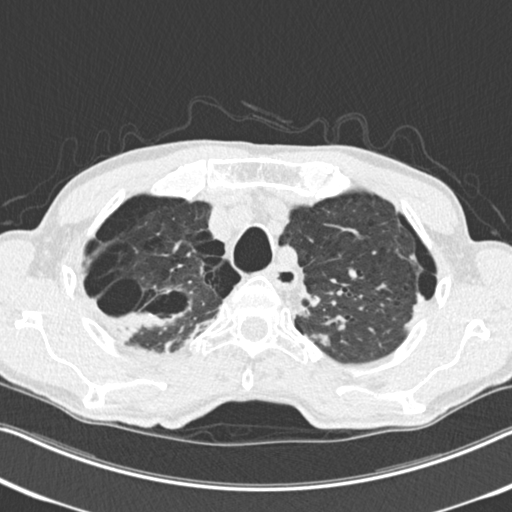
Low-dose screening chest CT, one axial slice; slice 206 of 251 in the series (ordered by position); reconstruction kernel B30f; lung window (W 1500 / L -600 HU); 2 mm slice thickness; 512 × 512 image matrix, field of view 334 × 334 mm.
Annotated regions visible in this slice (manually delineated by an expert):
- lesion 1 (tumor, upper lobe of right lung): bounding box (x1, y1, x2, y2) in pixels: (112, 312, 174, 340)